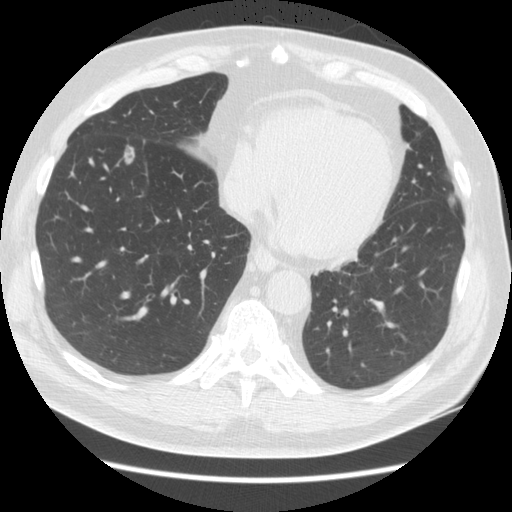
Low-dose screening chest CT, one axial slice. Slice 53 of 161 in the series (ordered by position). 140 kVp. Lung window (W 1500 / L -600 HU). 2.5 mm slice thickness. 512 × 512 image matrix.
Structures marked on this image (expert manual segmentation):
- lesion 1 (tumor, lower lobe of right lung): bounding box <124,145,135,164> (left, top, right, bottom; pixels)